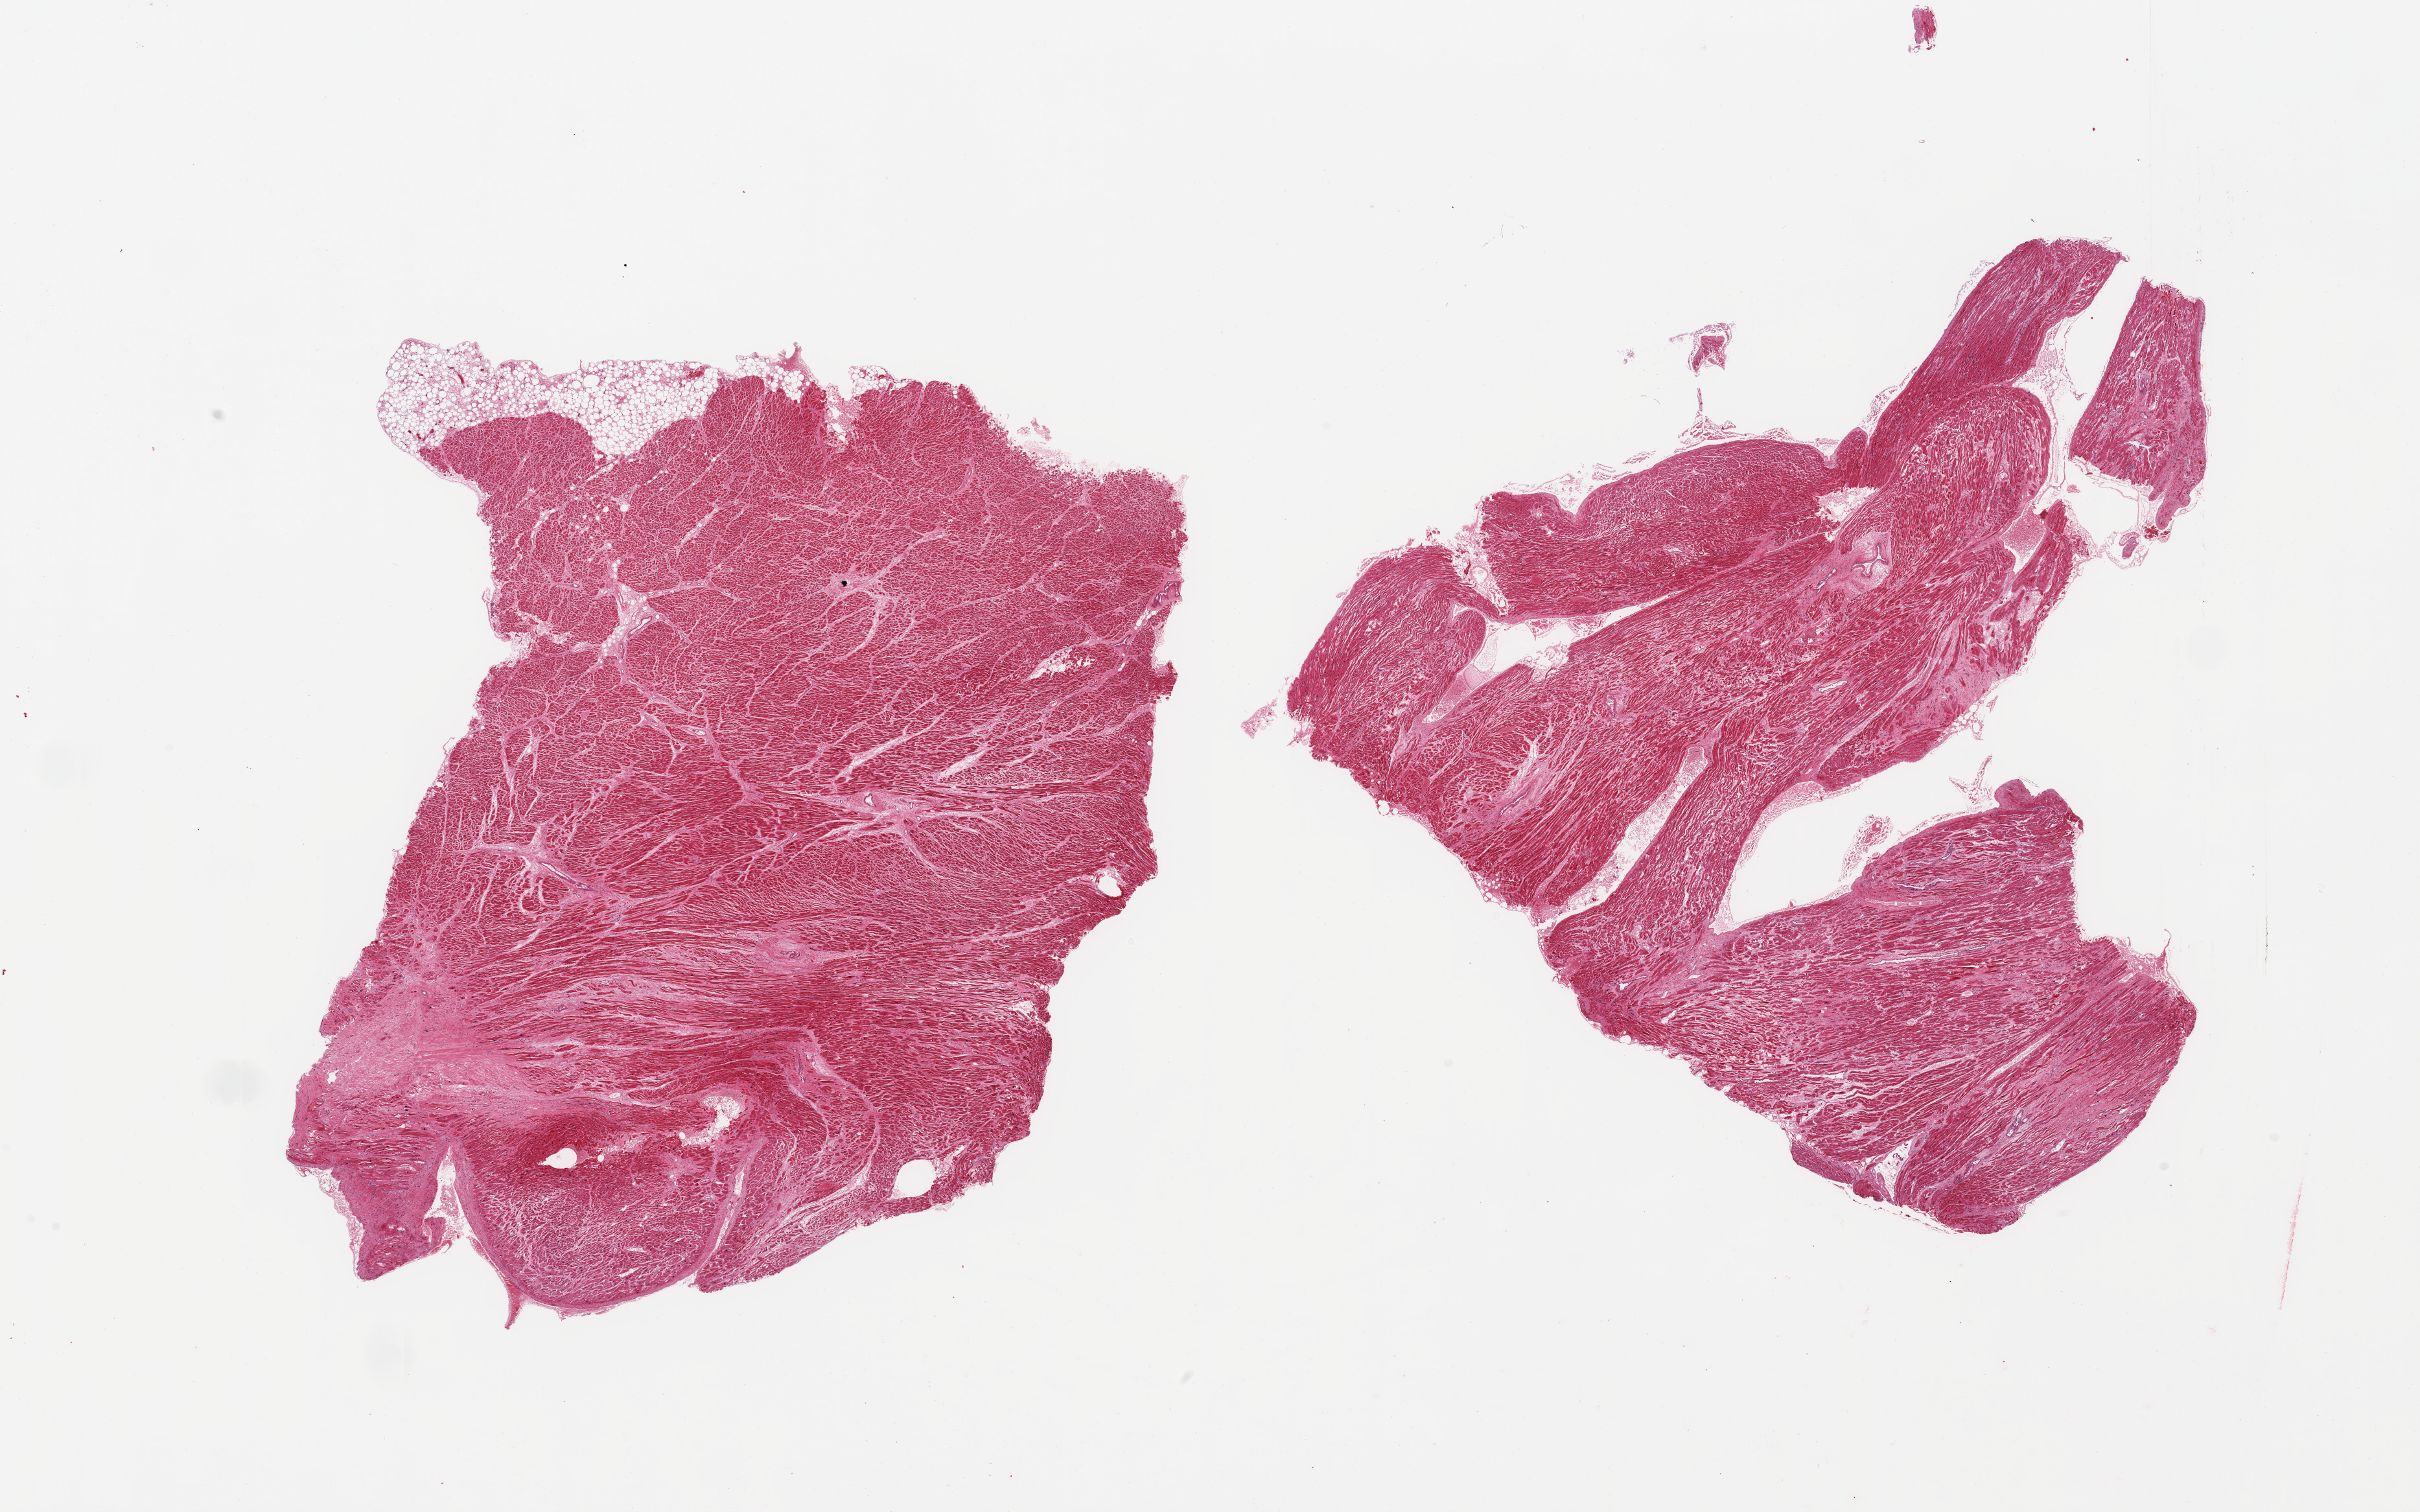
H&E whole-slide image — whole scanned area (about 29.5 x 18.5 mm) shown as a low-resolution overview. PAXgene-fixed paraffin-embedded (PFPE) section. Sampled site (target tissue): heart. Donor tissue sample. Donor: male.
- review note (as recorded): 2 pieces; interstitial fibrosis with scaring; multifocal hyalinization/ eosinophilia of fibers; rim of attached fat